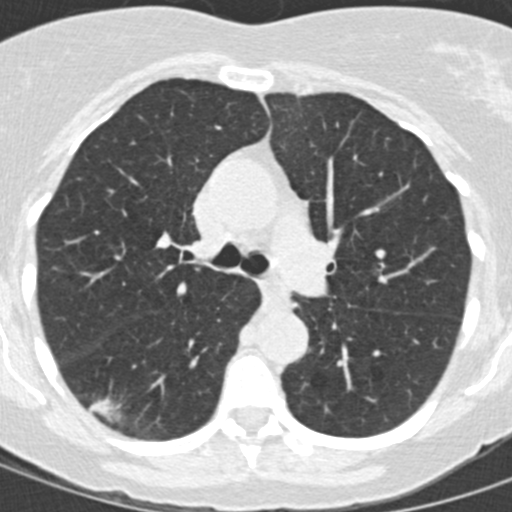
Low-dose screening chest CT, one axial slice. Reconstruction kernel B30f. 120 kVp. Lung window (W 1500 / L -600 HU). 2 mm slice thickness. 512 × 512 image matrix, field of view 270 × 270 mm.
Outlined on this slice (outlined manually by an expert reader):
- lesion 1 (tumor, lower lobe of right lung): box from (x=89, y=398) to (x=121, y=422) px